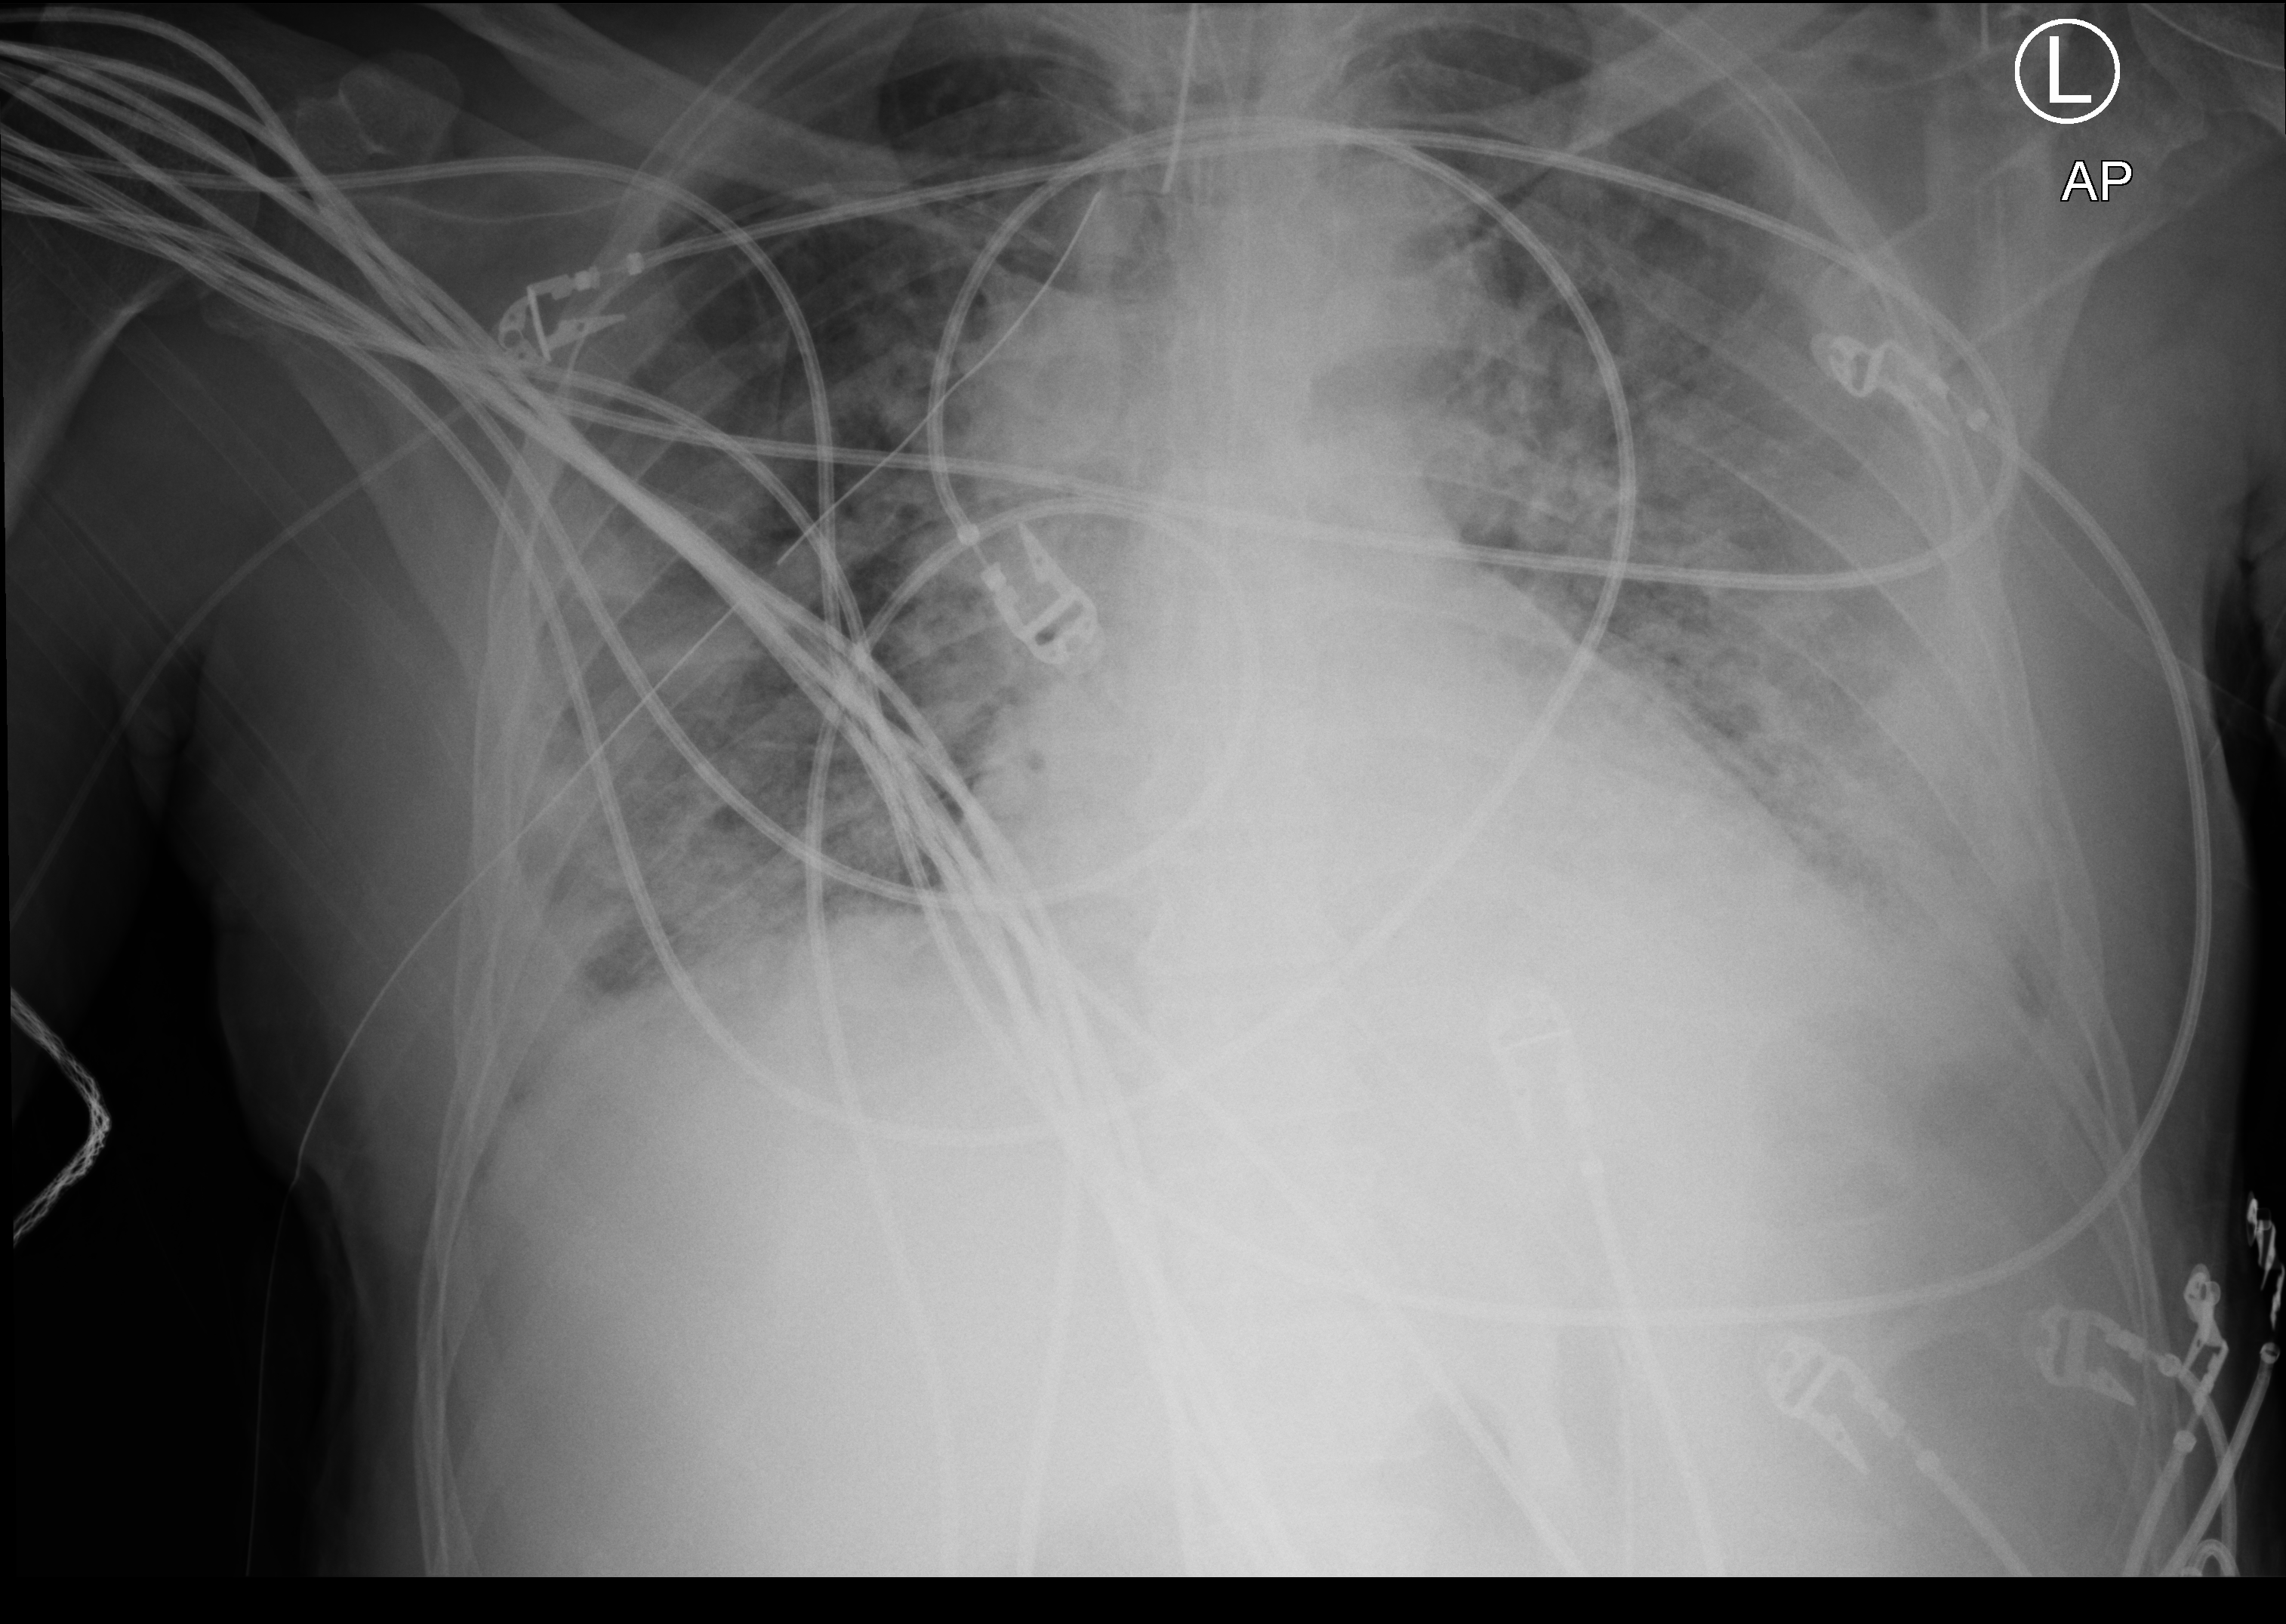
Portable chest radiograph; anteroposterior (AP) projection. Patient hospitalised with COVID-19; male, aged 18–59 years.
Hospital-stay facts (about this admission, not read from this image; timing relative to this image not recorded): admitted to intensive care during this hospital stay: yes.